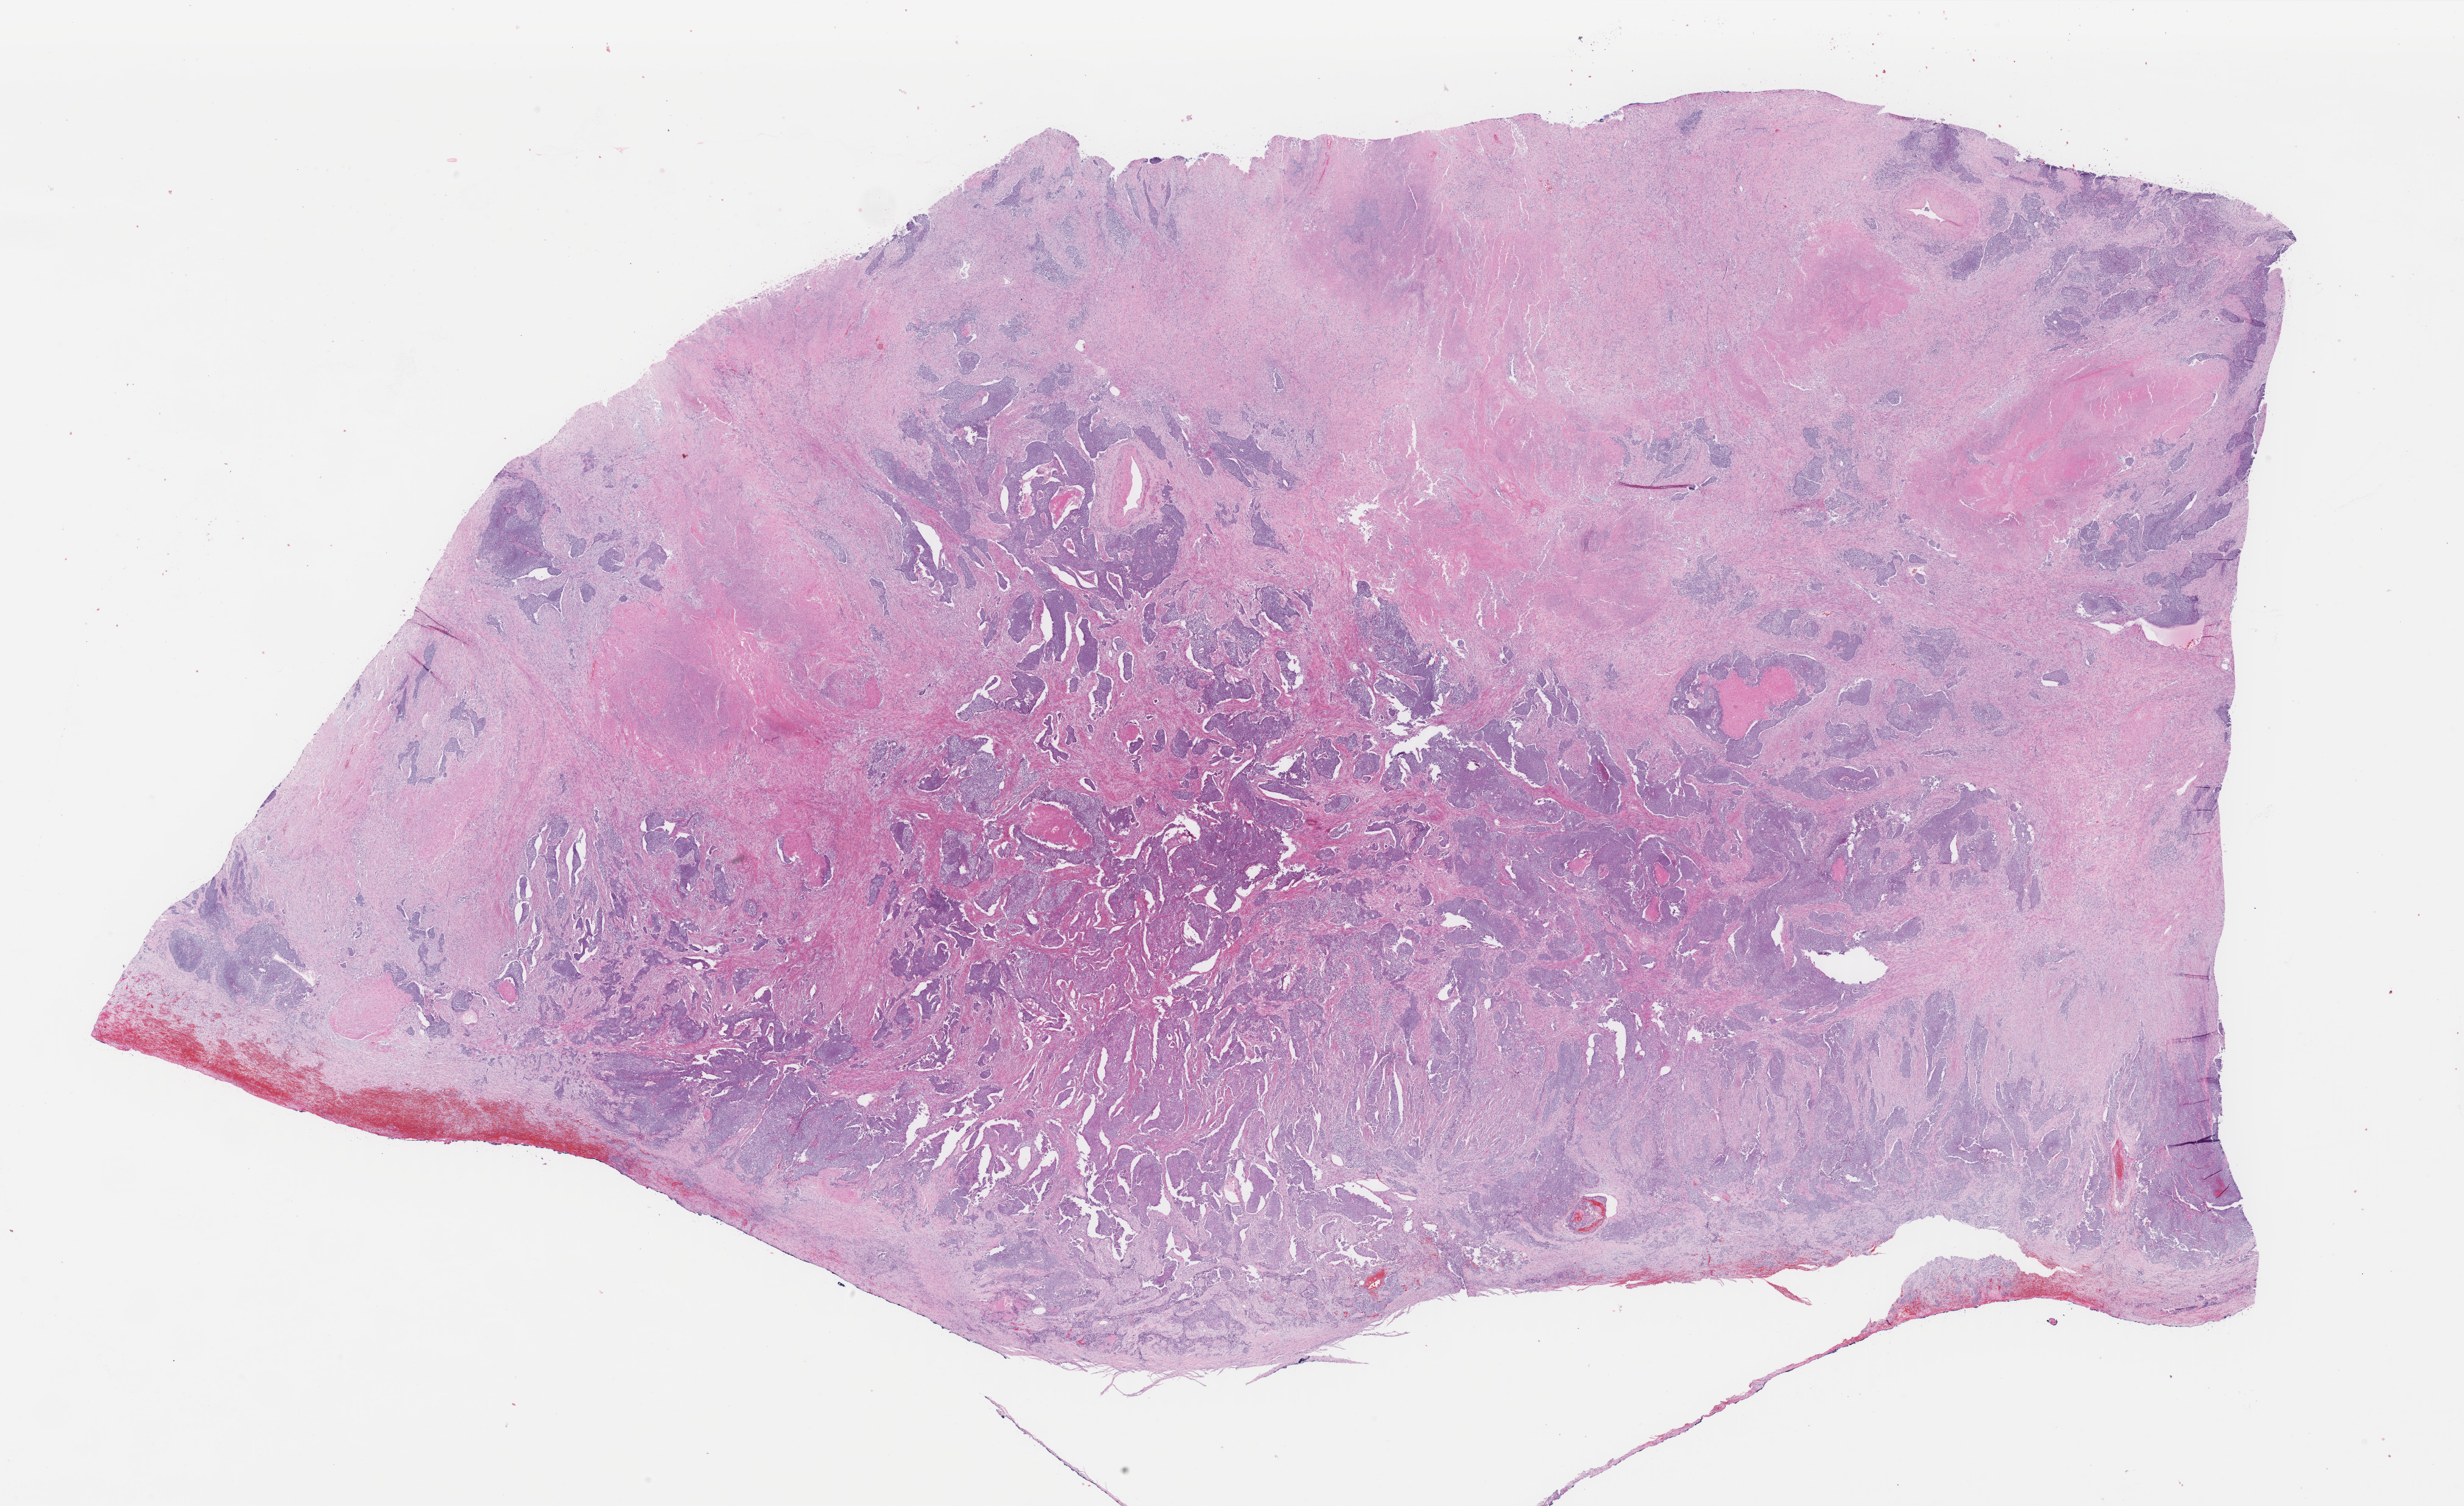
Whole-slide histology image, Hematoxylin and eosin (H&E) stained, whole scanned area (about 32.1 x 19.6 mm) shown as a low-resolution overview, formalin-fixed paraffin-embedded (FFPE) diagnostic section, sample: primary tumour, uterus. Female, age 50 years at initial diagnosis. Histologic grade: G3 (poorly differentiated).
• FIGO stage: IIIC1
• histologic diagnosis: Carcinoma, undifferentiated, NOS